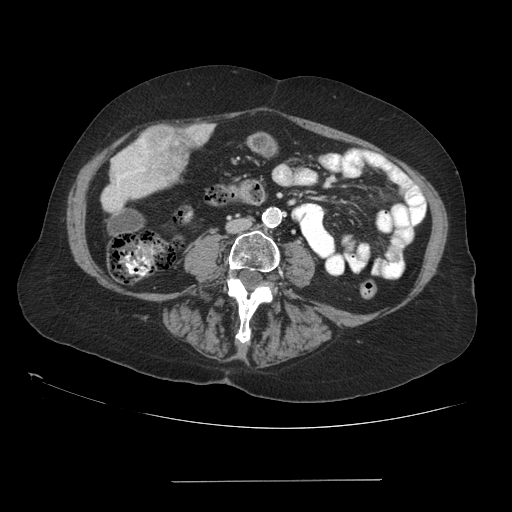
Contrast-enhanced abdominal CT (liver protocol), one axial slice; position 15 of 89 along the scan axis; reconstruction kernel STANDARD; soft-tissue window (W 400 / L 40 HU); 512 × 512 image matrix, field of view 400 × 400 mm. From the clinical record (not read from this slice): diagnosis: hepatocellular carcinoma (patient treated with transarterial chemoembolisation; whether this scan precedes or follows treatment is not stated here); TNM stage (as recorded): Stage-IVA; Child-Pugh class: A.
Outlined on this slice (semi-automatically segmented with operator editing):
- mass: bounding box [x1, y1, x2, y2] px = [134, 122, 215, 186]